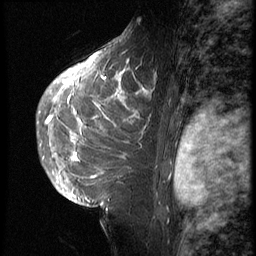
Breast MRI (dynamic contrast-enhanced), one sagittal slice; 3 images stored at this slice position (order not interpretable as contrast timing); 1.5 T; TE 4.2 ms, TR 9 ms; 2.5 mm slice thickness; 256 × 256 image matrix, field of view 180 × 180 mm. Female patient, age 28 years. Case-level facts recorded for this patient, not image findings: setting: breast cancer imaged before/during neoadjuvant chemotherapy.
Structures marked on this image (semi-automatic segmentation, software-assisted and operator-edited):
- analysis volume of interest (the breast-tissue region the enhancement analysis was run in; not a lesion): bounding box [x1, y1, x2, y2] px = [42, 45, 159, 207]
- tumour enhancement mask (voxels above the 140 % enhancement threshold inside the analysis volume of interest): [45, 52, 151, 178]